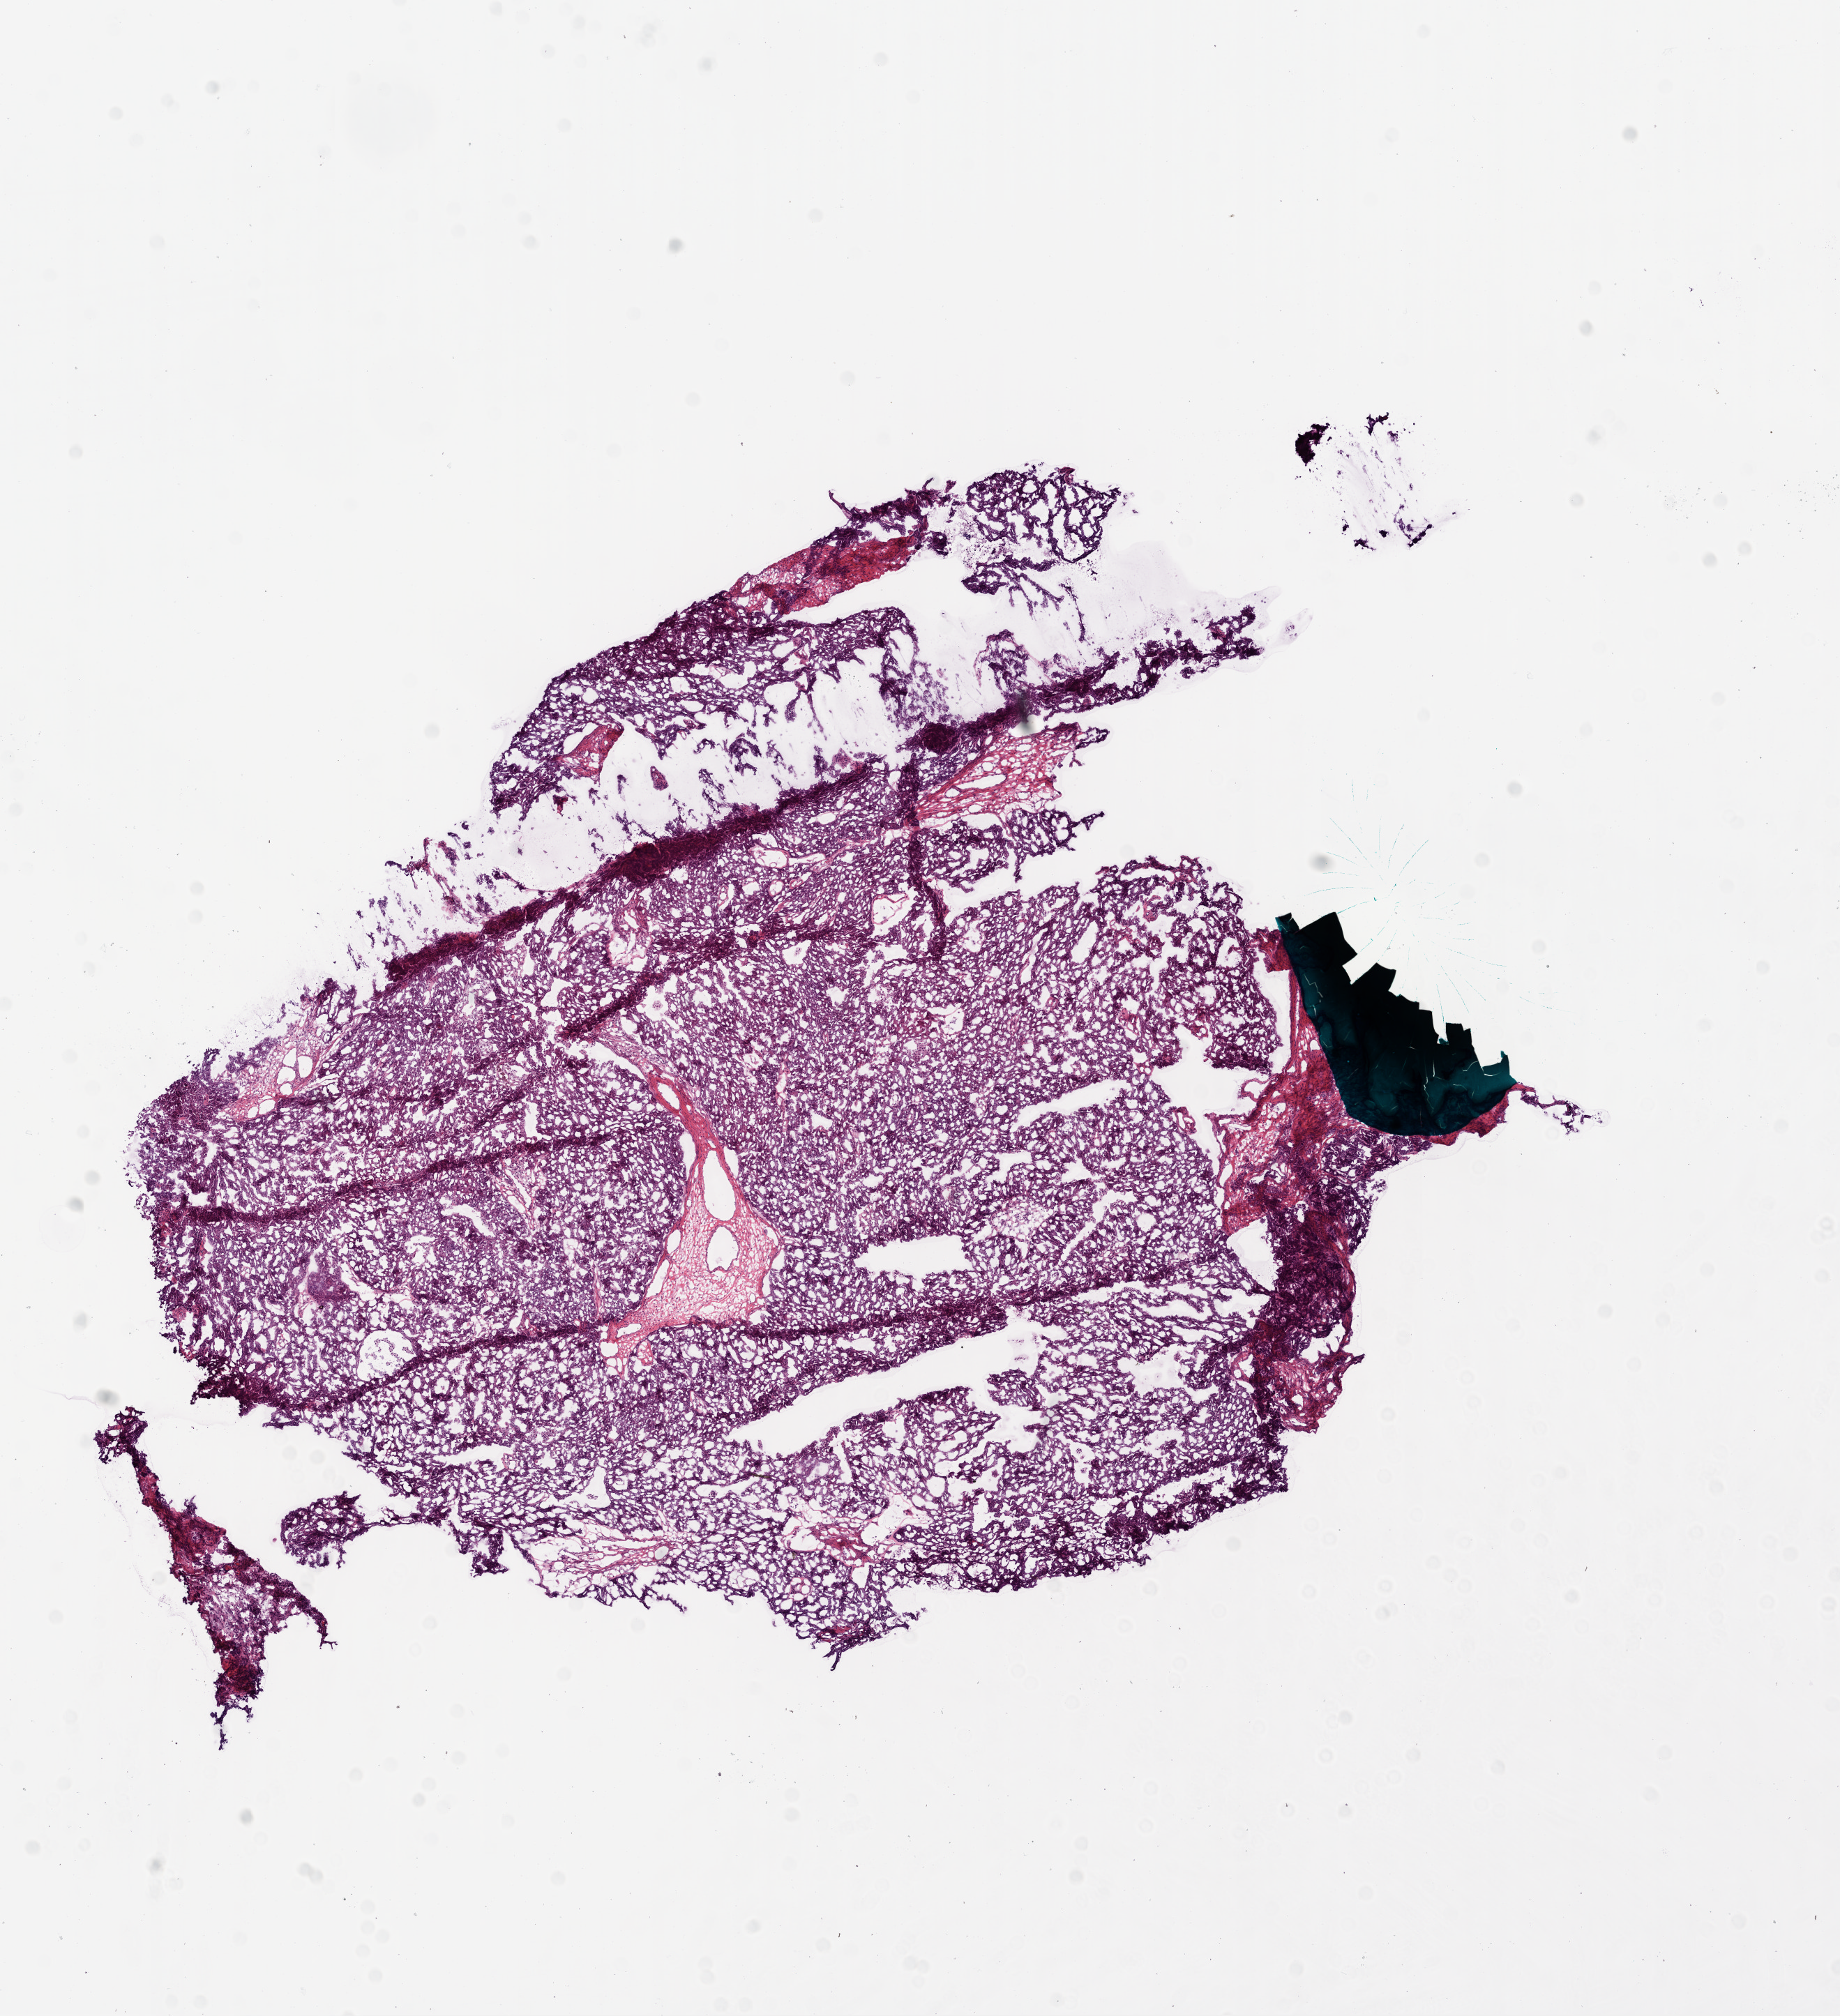
Whole-slide histology image, Hematoxylin and eosin (H&E) stained — a low-resolution overview of the entire scanned area, about 10.6 x 11.7 mm (acquisition: 20x scan). Frozen section from the bottom of the tissue portion. Sample: primary tumour, ovary. Female patient; age at initial diagnosis 50 years. Histologic grade: G3 (poorly differentiated). Composition of this section per pathologist review: tumour cells 90%, tumour nuclei 99%, normal cells 0%, stromal cells 5%, necrosis 5%.
FIGO stage: IIIC. Histologic diagnosis: Serous cystadenocarcinoma, NOS.